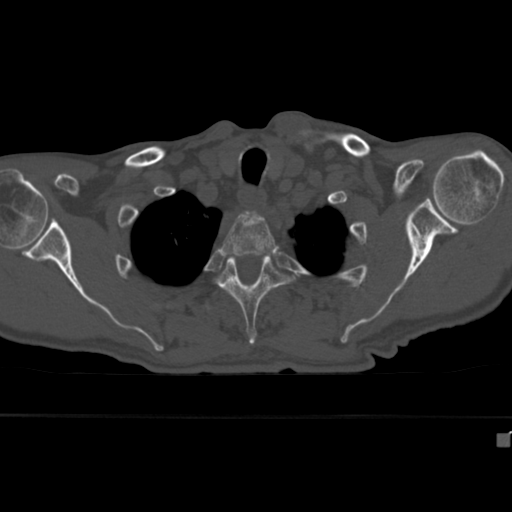
CT including the spine, one axial slice; position 335 of 430 along the scan axis; reconstruction kernel Br40s; 120 kVp; bone window (W 1800 / L 400 HU); 1.5 mm slice thickness; 512 × 512 image matrix, field of view 337 × 337 mm. Male patient, age 64 years. Case-level facts recorded for this patient, not image findings: primary cancer: uterus; vertebrae with lytic lesions (as recorded): T1, T4, T5, T7, L5.
Annotated regions visible in this slice (semi-automatically segmented with operator editing):
- T2 vertebra: bounding box [x1, y1, x2, y2] px = [218, 212, 279, 258]
- T3 vertebra: [215, 255, 295, 345]
- T4 vertebra: [204, 304, 211, 310]